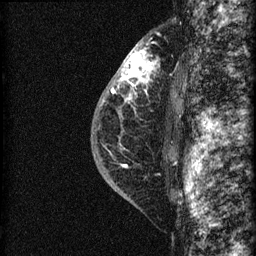
Breast MRI (dynamic contrast-enhanced), one sagittal slice. Slice 44 of 60 in the series (ordered by position). Dynamic contrast-enhanced series, image 2 of 3 at this slice position (ordered by acquisition). 1.5 T. TE 4.2 ms, TR 22.7 ms. 1.5 mm slice thickness. 256 × 256 image matrix. Female patient, age 48 years. From the clinical record (not read from this slice): setting: breast cancer imaged before/during neoadjuvant chemotherapy; receptor status: triple-negative.
Structures marked on this image (semi-automatically segmented with operator editing):
- analysis volume of interest (the breast-tissue region the enhancement analysis was run in; not a lesion): bounding box (x1, y1, x2, y2) in pixels: (115, 34, 169, 162)
- tumour enhancement mask (voxels above the 90 % enhancement threshold inside the analysis volume of interest): (118, 48, 154, 101)